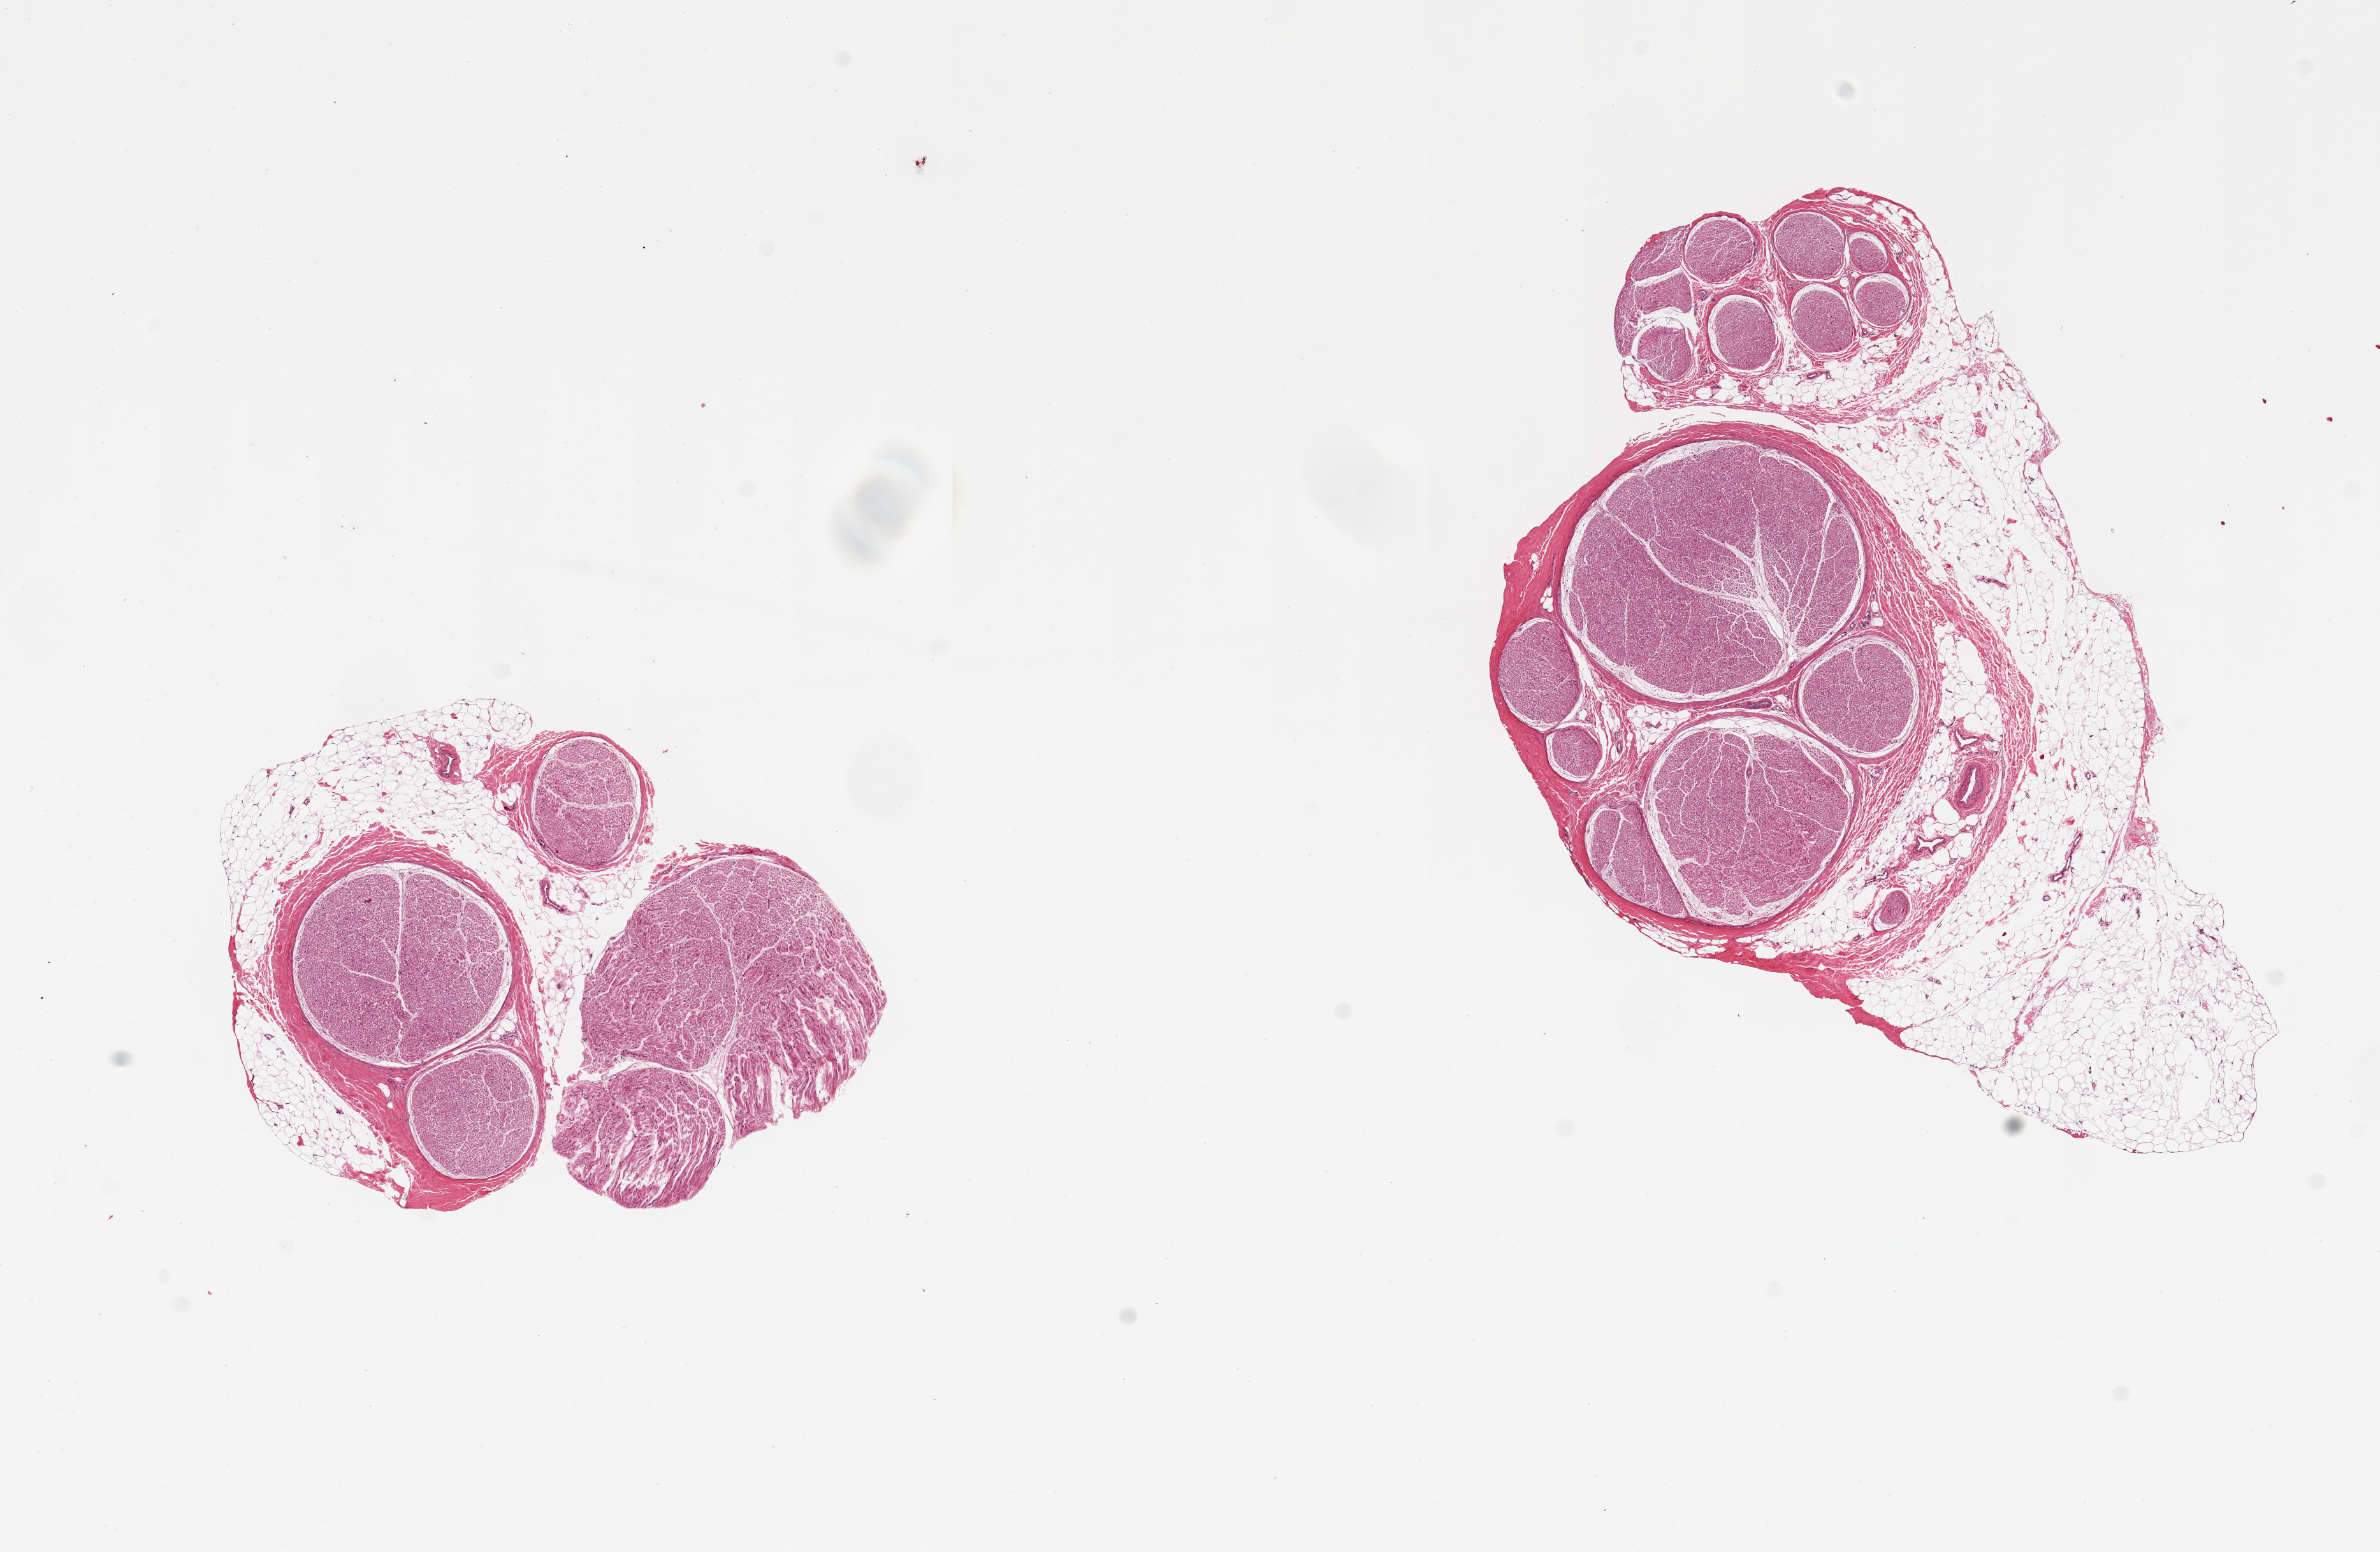
Digitized H&E-stained section — whole scanned area (about 14.8 x 9.6 mm, slide scanned at 20x) shown as a low-resolution overview, PAXgene-fixed, paraffin-embedded tissue, target tissue: tibial nerve, tissue donor sample.
Review note (as recorded): 2 pieces, partial rim of adherent fat up to ~3mm.